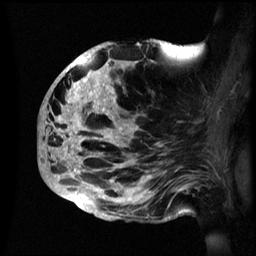
Breast MRI (dynamic contrast-enhanced), one sagittal slice; position 30 of 60 along the scan axis; dynamic contrast-enhanced series, image 2 of 3 at this slice position (ordered by acquisition); 1.5 T; TE 4.2 ms, TR 8.4 ms; 2.4 mm slice thickness; 256 × 256 image matrix, field of view 230 × 230 mm. Patient: female, 48 years.
Outlined on this slice (semi-automatic segmentation, software-assisted and operator-edited):
- analysis volume of interest (the breast-tissue region the enhancement analysis was run in; not a lesion): bounding box <39,41,195,222> (left, top, right, bottom; pixels)
- tumour enhancement mask (voxels above the 70 % enhancement threshold inside the analysis volume of interest): <39,43,170,214>